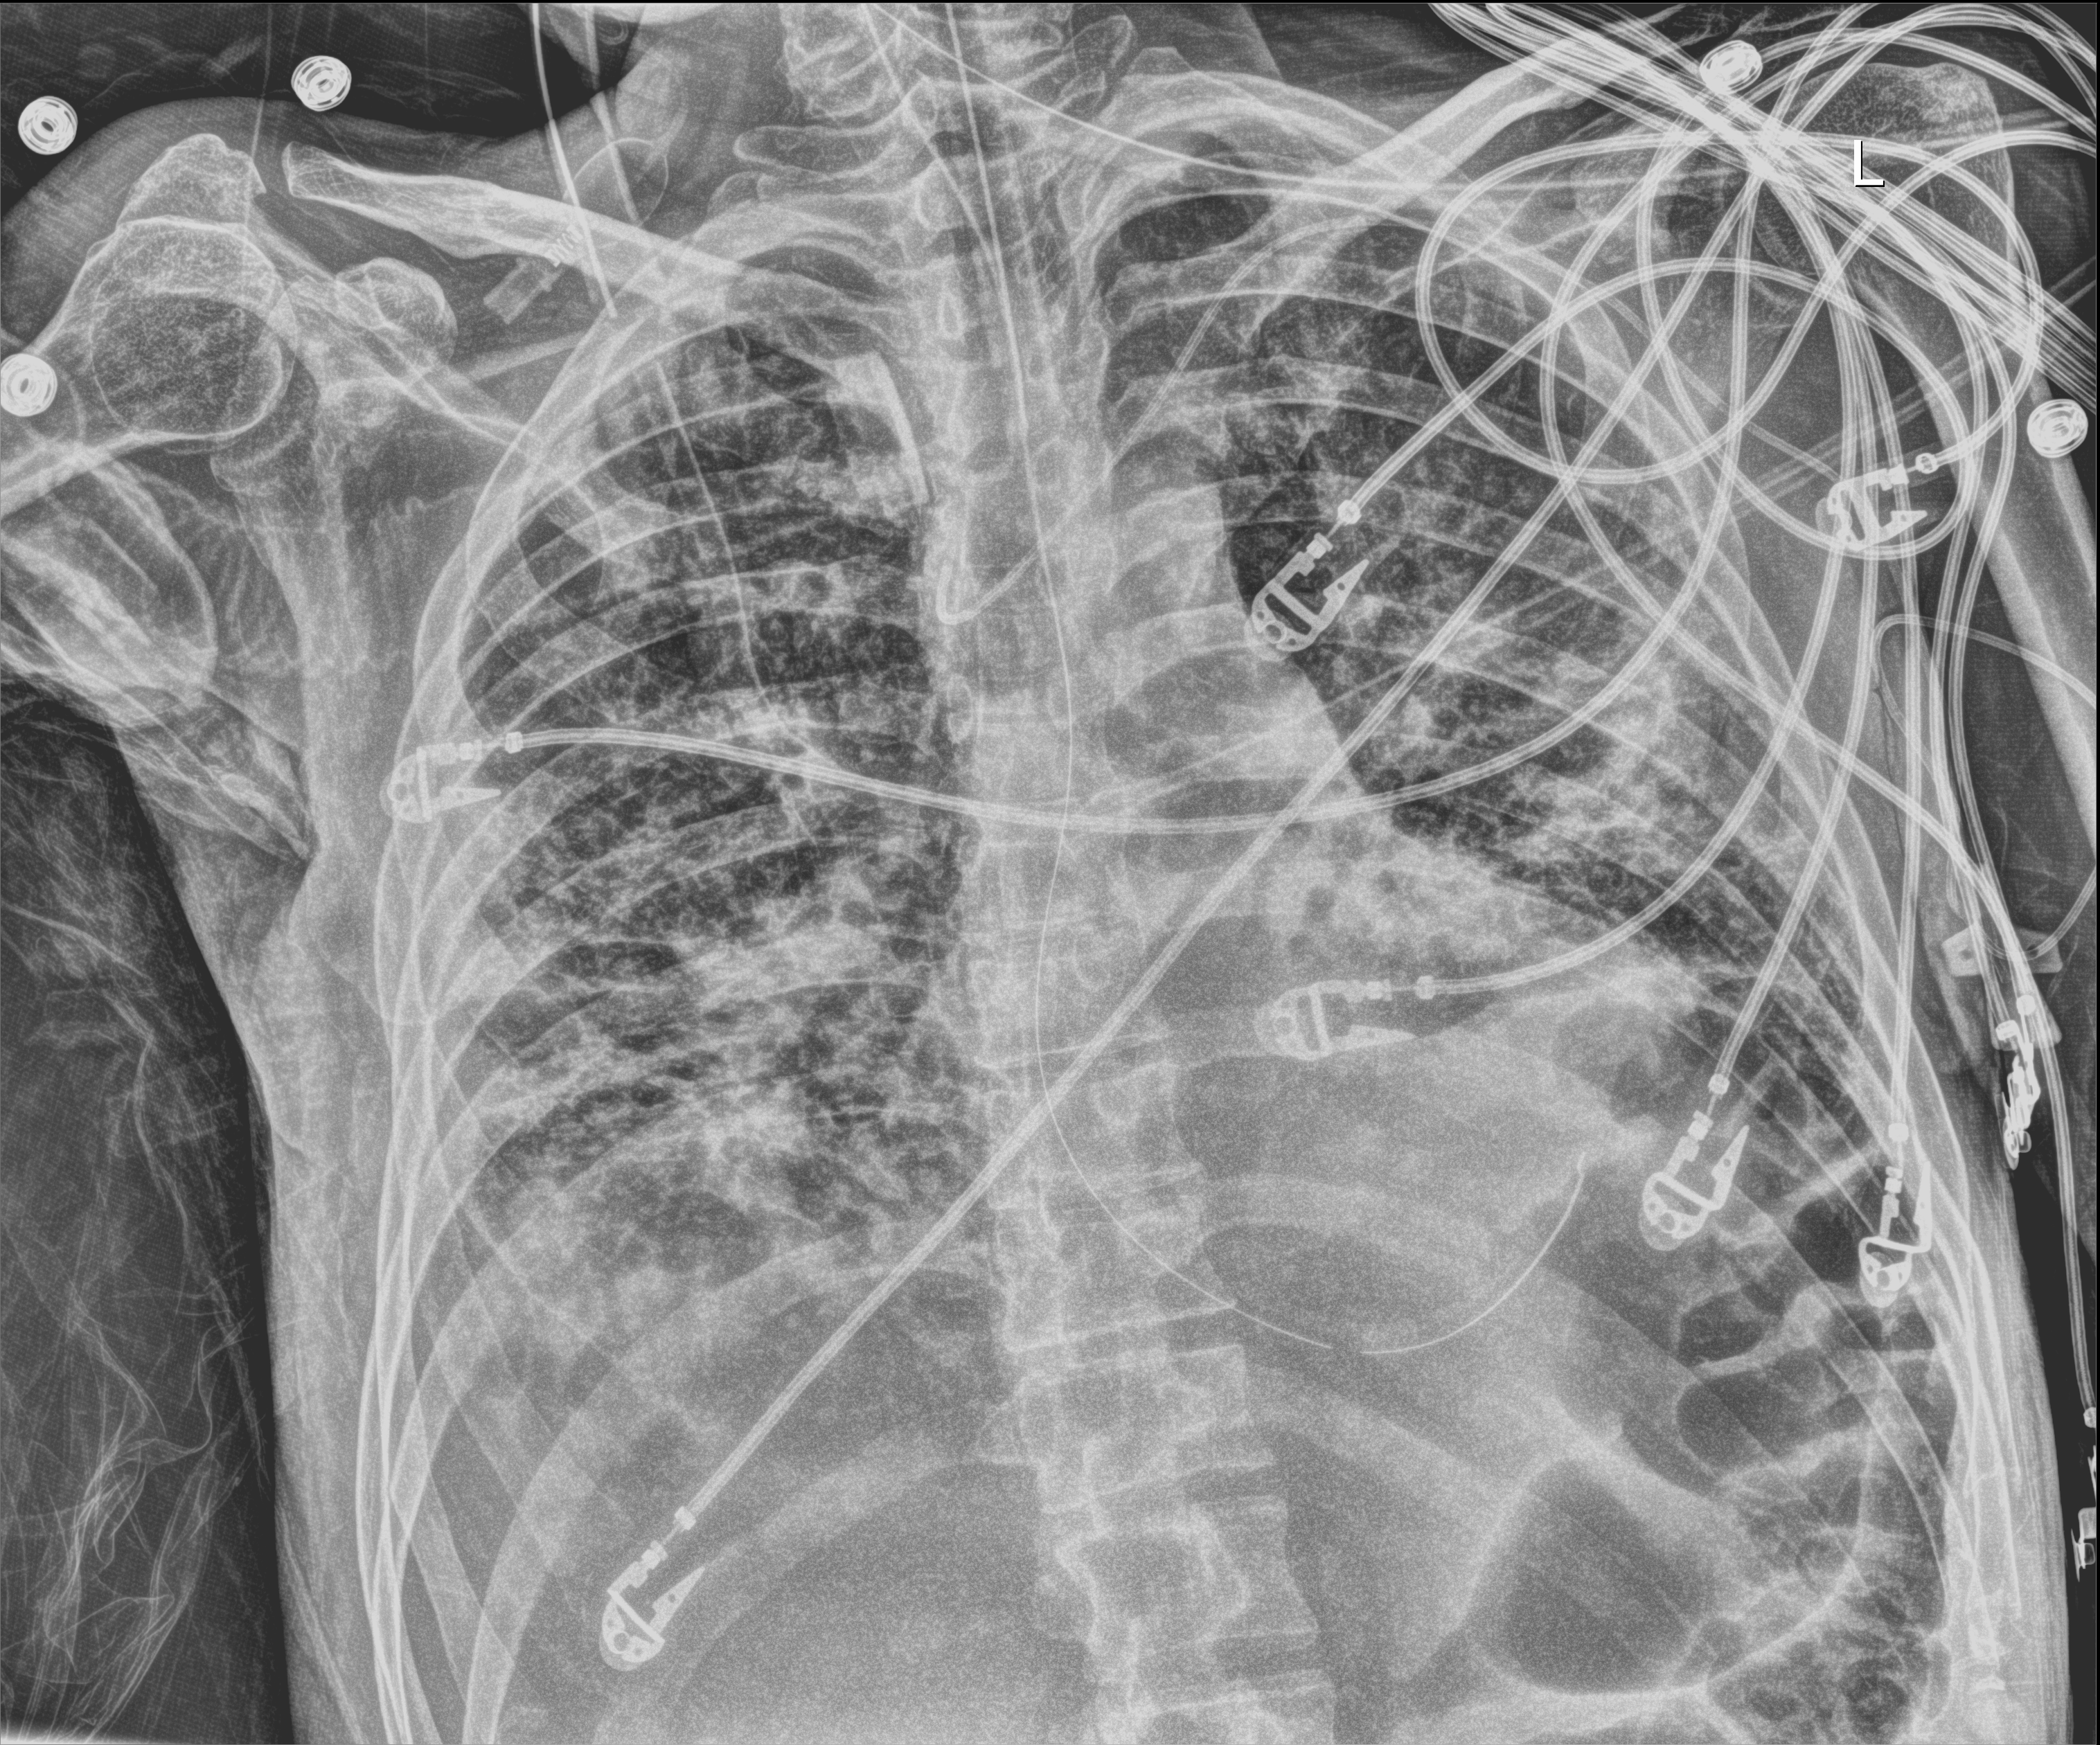
Chest X-ray (portable); anteroposterior (AP) projection. Patient hospitalised with COVID-19; male, aged 18–59 years.
Hospital-stay facts (about this admission, not read from this image; timing relative to this image not recorded):
- admitted to intensive care during this hospital stay: yes